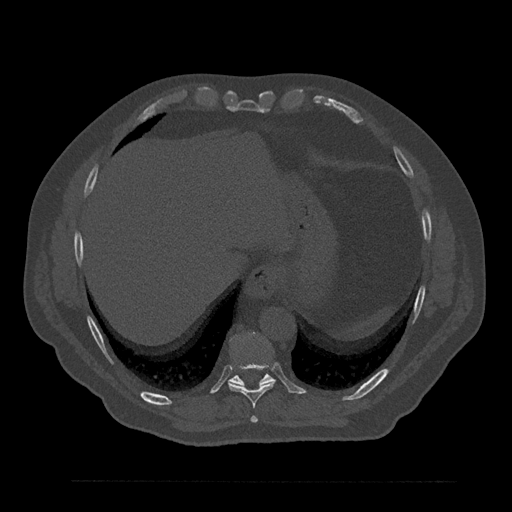
CT including the spine, one axial slice. Position 386 of 797 along the scan axis. 120 kVp. Bone window (W 1800 / L 400 HU). 0.5 mm slice thickness. 512 × 512 image matrix, field of view 430 × 430 mm. Male patient, age 61 years. From the clinical record (not read from this slice): primary cancer: prostate.
Outlined on this slice (semi-automatic segmentation, software-assisted and operator-edited):
- T10 vertebra: bounding box (x1, y1, x2, y2) in pixels: (228, 332, 274, 385)
- T8 vertebra: (250, 416, 258, 423)
- T9 vertebra: (228, 364, 275, 408)